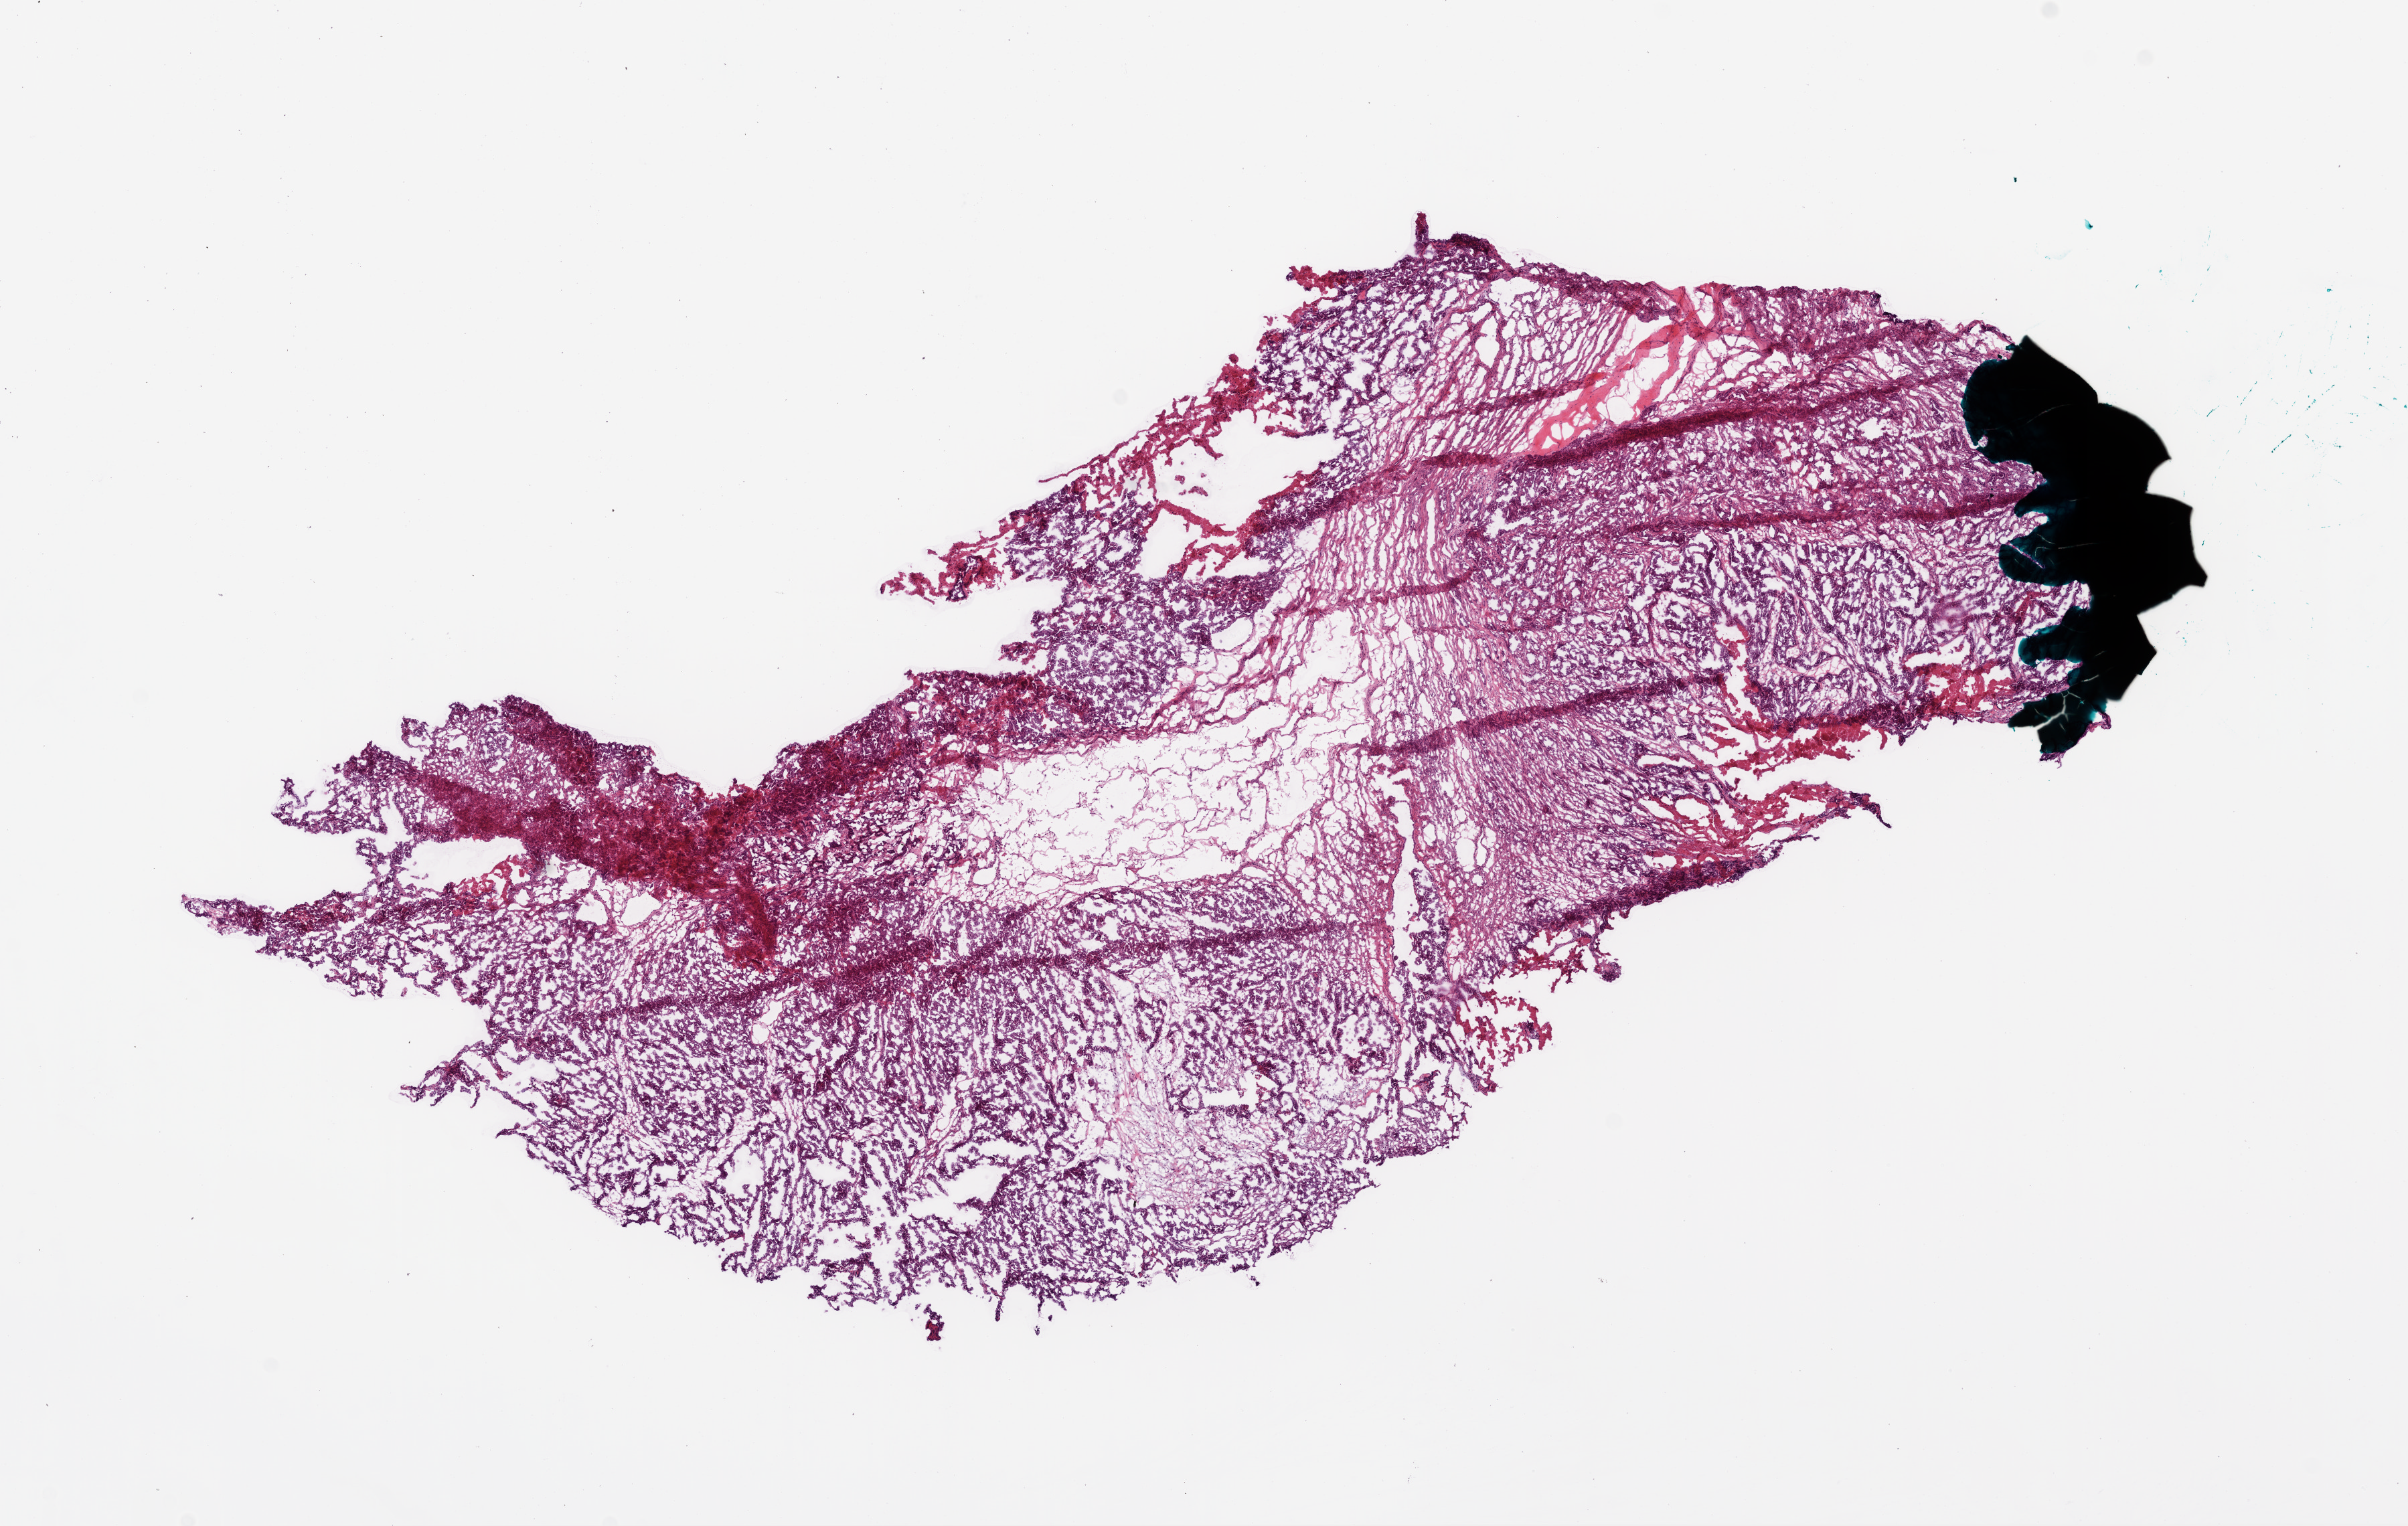
Digitized Hematoxylin and eosin (H&E) stained tissue section (whole slide) — whole scanned area (about 14.5 x 9.2 mm, from a 20x scan) shown as a low-resolution overview, frozen section from the bottom of the tissue portion, sample: primary tumour, ovary. Female patient; age at initial diagnosis 77 years. Histologic grade: G3 (poorly differentiated). Composition of this section per pathologist review: tumour cells 65%, tumour nuclei 75%, normal cells 0%, stromal cells 35%, necrosis 0%.
Laterality: bilateral. Pathologic diagnosis: Serous cystadenocarcinoma, NOS. FIGO stage: IIIC.